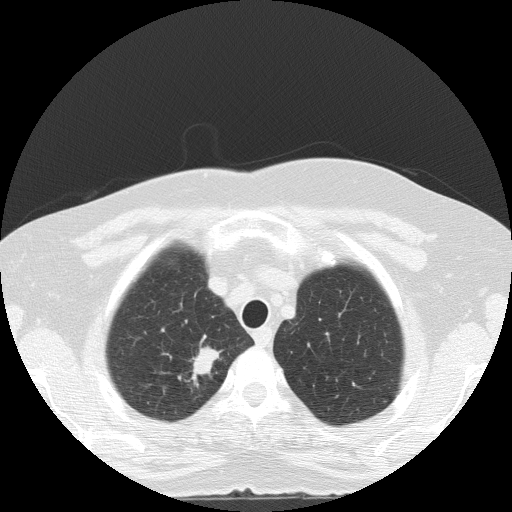
Axial slice from a low-dose chest CT screening exam; first (baseline) screen; lung window (W 1500 / L -600 HU); 2 mm slice thickness; lung (sharp) reconstruction kernel (FC51). Female, age 56 years at enrolment. Current smoker at enrolment.
Expert reader's lesion annotation, box from (x=172, y=342) to (x=231, y=389) px. The screening reader recorded 2 non-calcified nodules or masses ≥4 mm on this exam (right upper lobe, right lower lobe); which of them this box marks is not recorded. Official screen result: positive, change unspecified: nodule(s) >= 4 mm or enlarging nodule(s), mass(es), or other non-specific abnormalities suspicious for lung cancer. Participant outcome: lung cancer diagnosed 24 days after this screen — adenocarcinoma, NOS, right upper lobe, poorly differentiated (G3), stage IA (AJCC 6th edition), 20 mm at pathology.